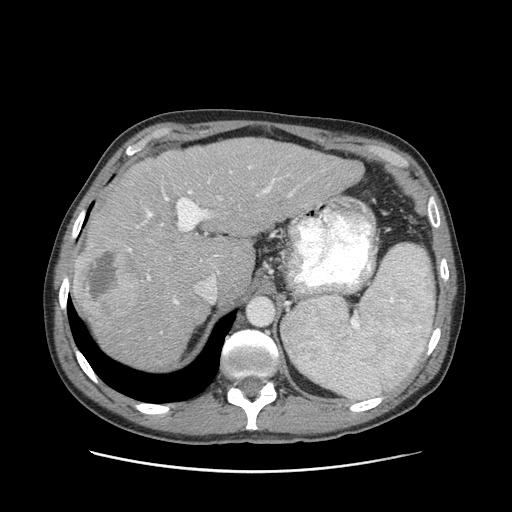
Contrast-enhanced abdominal CT (liver protocol), one axial slice. Slice 69 of 93 in the series (ordered by position). Reconstruction kernel STANDARD. Soft-tissue window (W 400 / L 40 HU). 2.5 mm slice thickness. 512 × 512 image matrix, field of view 380 × 380 mm. From the clinical record (not read from this slice): diagnosis: hepatocellular carcinoma (patient treated with transarterial chemoembolisation; whether this scan precedes or follows treatment is not stated here); TNM stage (as recorded): Stage-II; Child-Pugh class: A; tumour differentiation: moderately differentiated; tumour size: 1 cm.
Annotated regions visible in this slice (semi-automatic segmentation, software-assisted and operator-edited):
- liver parenchyma outside the tumour (the mass and vessels are separate outlines, so this box may not span the whole liver): bounding box (x1, y1, x2, y2) in pixels: (72, 138, 362, 368)
- mass: (74, 243, 141, 320)
- liver vessels: (129, 166, 292, 305)